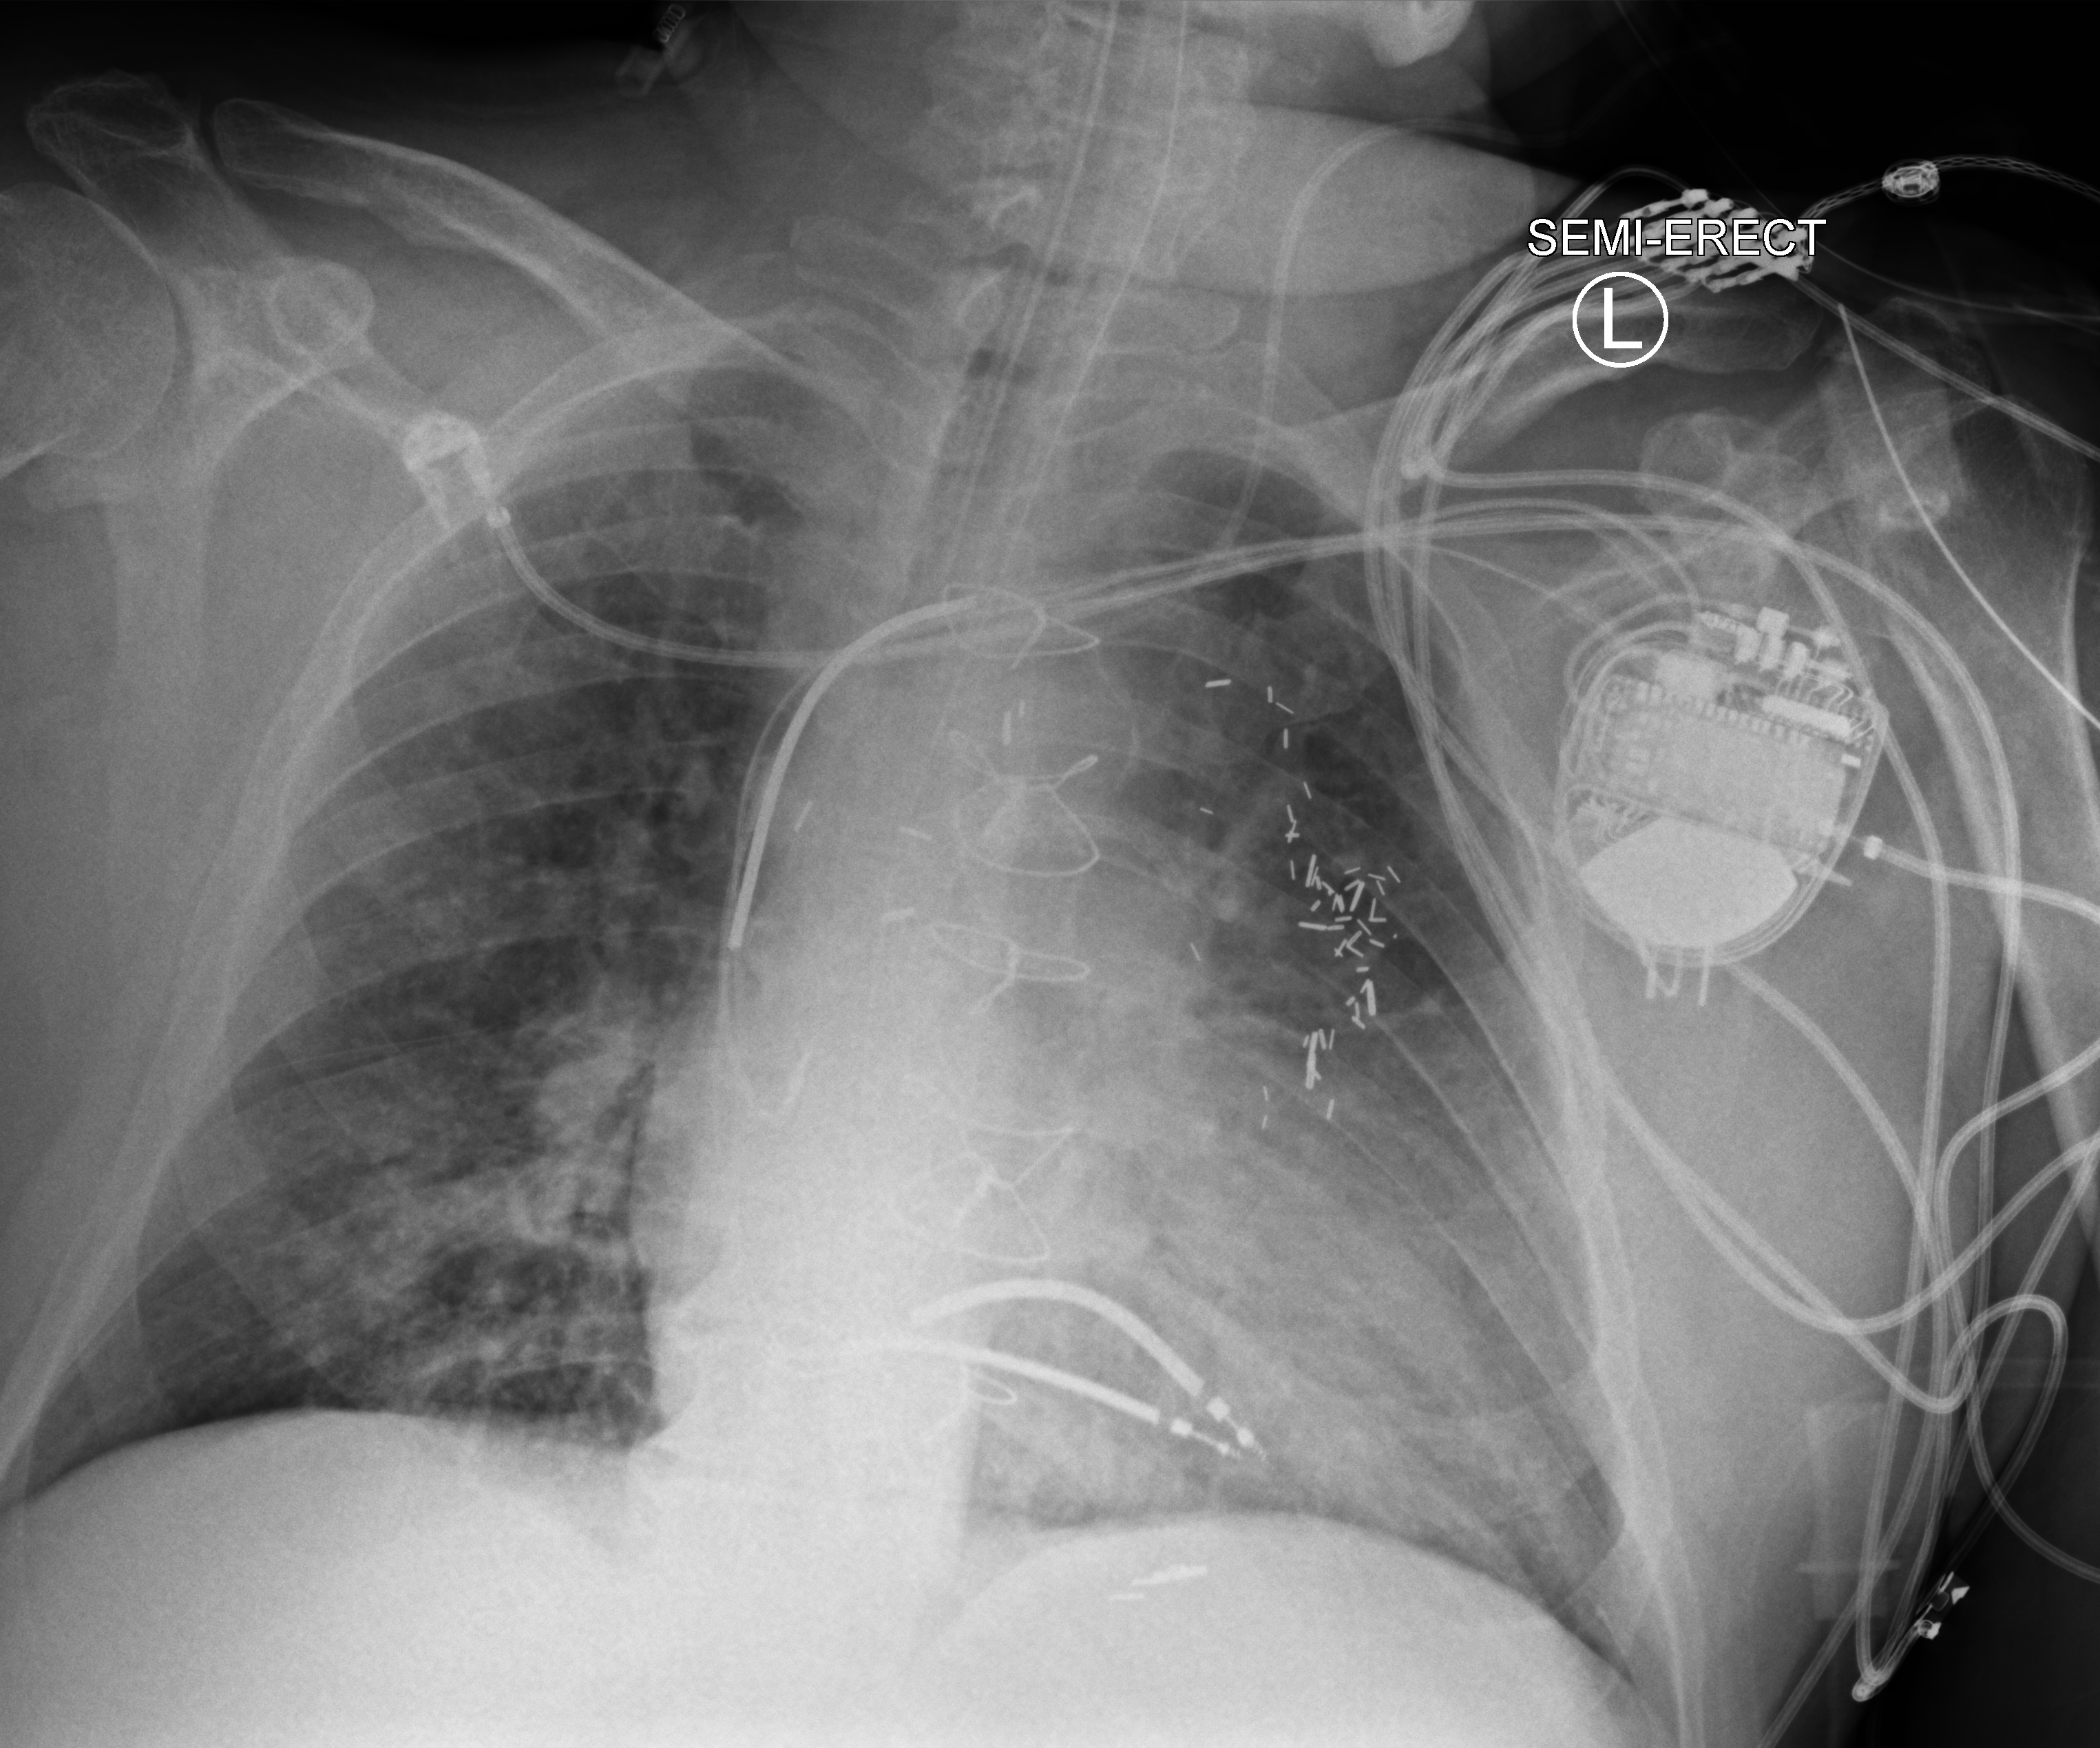
Chest X-ray (portable); anteroposterior (AP) projection. Patient hospitalised with COVID-19; male, aged 60–74 years.
From the hospital-stay record, not from the radiograph (when in the stay this image was taken is not recorded):
- mechanically ventilated during this hospital stay: yes
- length of hospital stay: 55 days
- admitted to intensive care during this hospital stay: yes